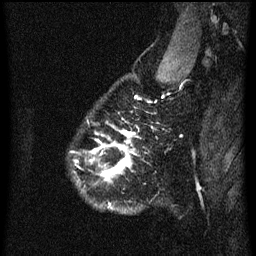
Breast MRI (dynamic contrast-enhanced), one sagittal slice; position 54 of 60 along the scan axis; dynamic contrast-enhanced series, image 2 of 3 at this slice position (ordered by acquisition); 1.5 T; TE 4.2 ms, TR 8.4 ms; 256 × 256 image matrix, field of view 180 × 180 mm. Female patient, age 34 years. Case-level facts recorded for this patient, not image findings: setting: breast cancer imaged before/during neoadjuvant chemotherapy; receptor status: HR-positive, HER2-negative.
Outlined on this slice (semi-automatically segmented with operator editing):
- analysis volume of interest (the breast-tissue region the enhancement analysis was run in; not a lesion): bounding box [x1, y1, x2, y2] px = [74, 58, 173, 215]
- tumour enhancement mask (voxels above the 70 % enhancement threshold inside the analysis volume of interest): [94, 130, 135, 181]